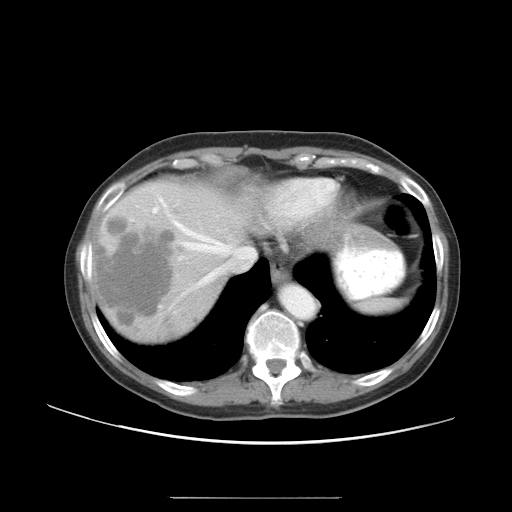
Contrast-enhanced abdominal CT, one axial slice. Slice 40 of 50 in the series (ordered by position). Reconstruction kernel STANDARD. Intravenous contrast given. Soft-tissue window (W 400 / L 40 HU). 512 × 512 image matrix, field of view 389 × 389 mm. Female patient, age 58 years. Case-level facts recorded for this patient, not image findings: diagnosis: colorectal cancer liver metastases, imaged before liver resection.
Structures marked on this image (outlined manually by an expert reader):
- hepatic veins: bounding box [x1, y1, x2, y2] px = [158, 197, 256, 285]
- liver: [95, 182, 244, 340]
- planned liver remnant (the part of the liver to remain after resection): [196, 186, 244, 243]
- portal vein (with intrahepatic branches): [152, 206, 159, 214]
- liver metastasis: [96, 220, 175, 327]